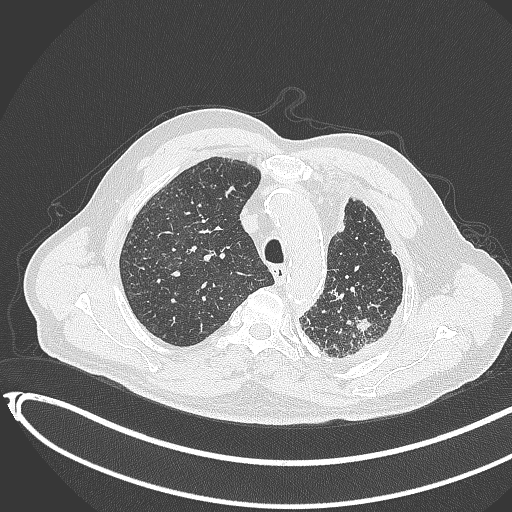
Chest CT, one axial slice; position 334 of 451 along the scan axis; 120 kVp; lung window (W 1500 / L -600 HU); 512 × 512 image matrix, field of view 400 × 400 mm. Patient: male, 78 years. Case-level facts recorded for this patient, not image findings: clinical TNM (as recorded): T1c N0 M1.
Annotated regions visible in this slice (bounding box drawn by a radiologist):
- lung tumour (recorded histology: adenocarcinoma): box from (x=353, y=311) to (x=377, y=335) px